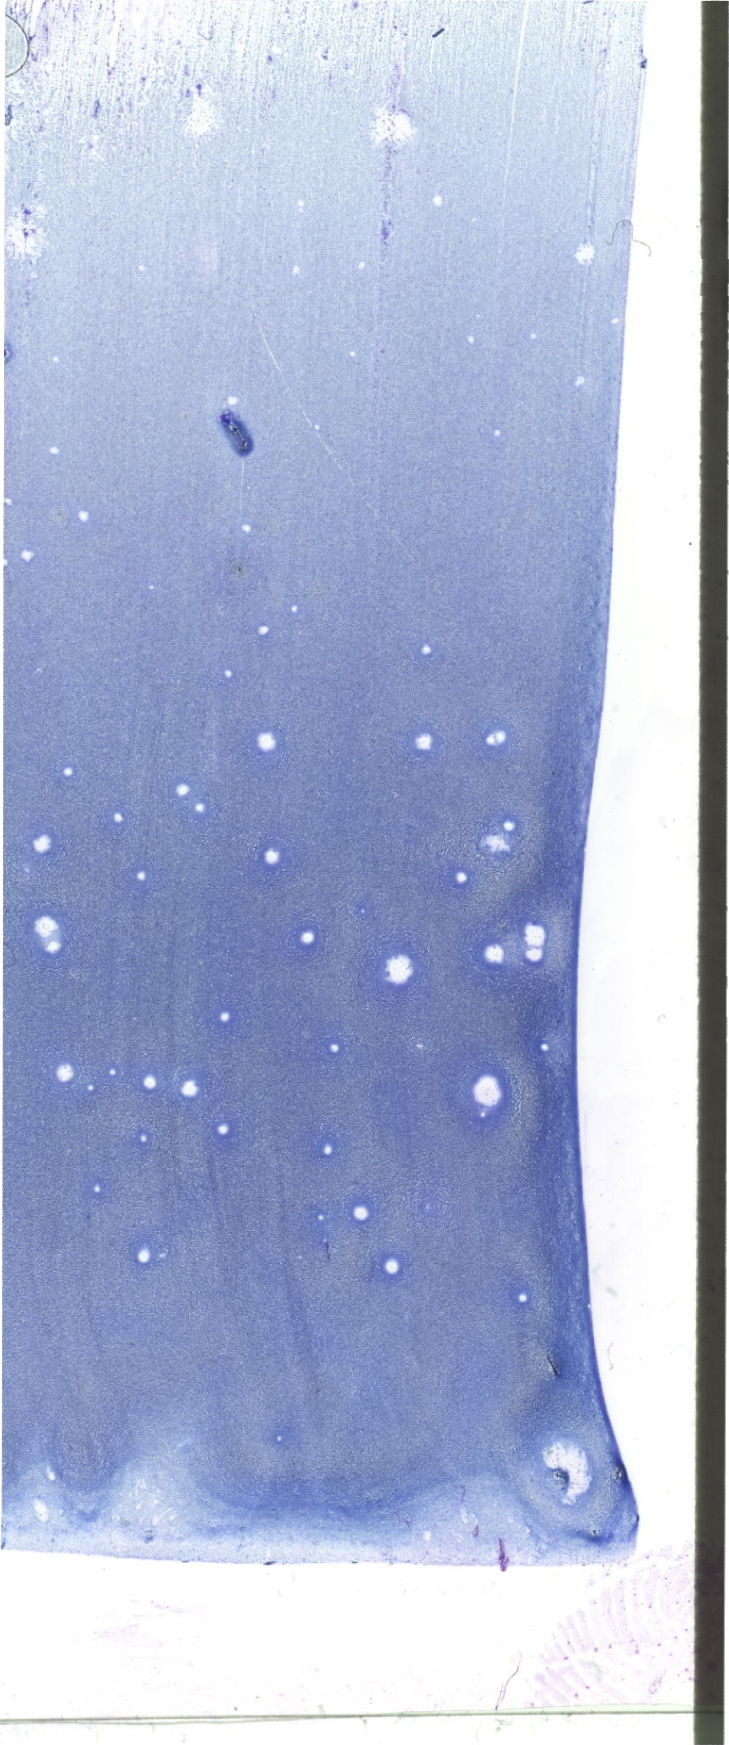
Whole-slide image of a May-Grünwald–Giemsa-stained bone marrow aspirate smear — whole scanned area (about 20.7 x 49.5 mm) shown as a low-resolution overview. Patient sex: male.
Diagnosis: Acute Monocytic Leukemia.